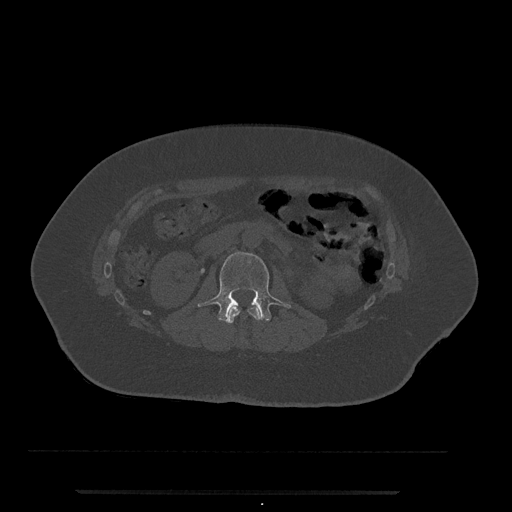
CT including the spine, one axial slice; position 51 of 797 along the scan axis; reconstruction kernel Br40s/3; bone window (W 1800 / L 400 HU); 0.5 mm slice thickness; 512 × 512 image matrix, field of view 440 × 440 mm. Female patient, age 51 years. Case-level facts recorded for this patient, not image findings: primary cancer: neuro.
Outlined on this slice (semi-automatic segmentation, software-assisted and operator-edited):
- L1 vertebra: bounding box <225,306,261,324> (left, top, right, bottom; pixels)
- L2 vertebra: <198,251,291,322>